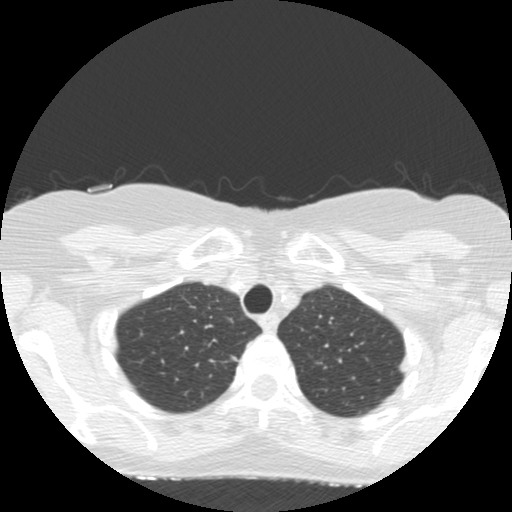
Low-dose screening chest CT, one axial slice; slice 129 of 155 in the series (ordered by position); reconstruction kernel STANDARD; lung window (W 1500 / L -600 HU); 2.5 mm slice thickness; 512 × 512 image matrix, field of view 300 × 300 mm.
Structures marked on this image (outlined manually by an expert reader):
- lesion 1 (tumor, upper lobe of right lung): bounding box <231,356,240,363> (left, top, right, bottom; pixels)